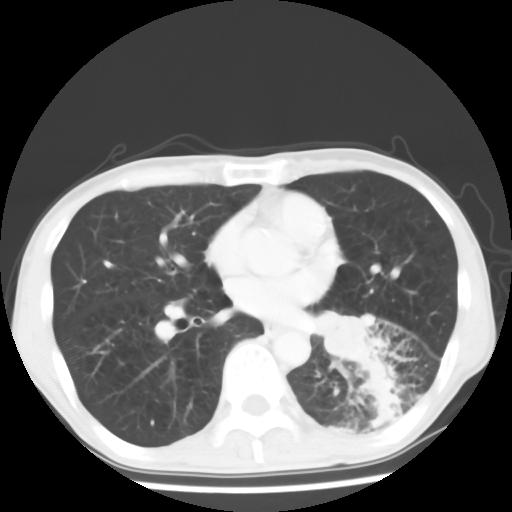
Chest CT, one axial slice; reconstruction kernel STANDARD; 120 kVp; lung window (W 1500 / L -600 HU); 5 mm slice thickness; 512 × 512 image matrix, field of view 313 × 313 mm. Patient: male, 68 years. Case-level facts recorded for this patient, not image findings: clinical TNM (as recorded): T4 N0 M0.
Annotated regions visible in this slice (rectangle marked by the reading radiologist):
- lung tumour (recorded histology: squamous cell carcinoma): box from (x=306, y=300) to (x=381, y=371) px